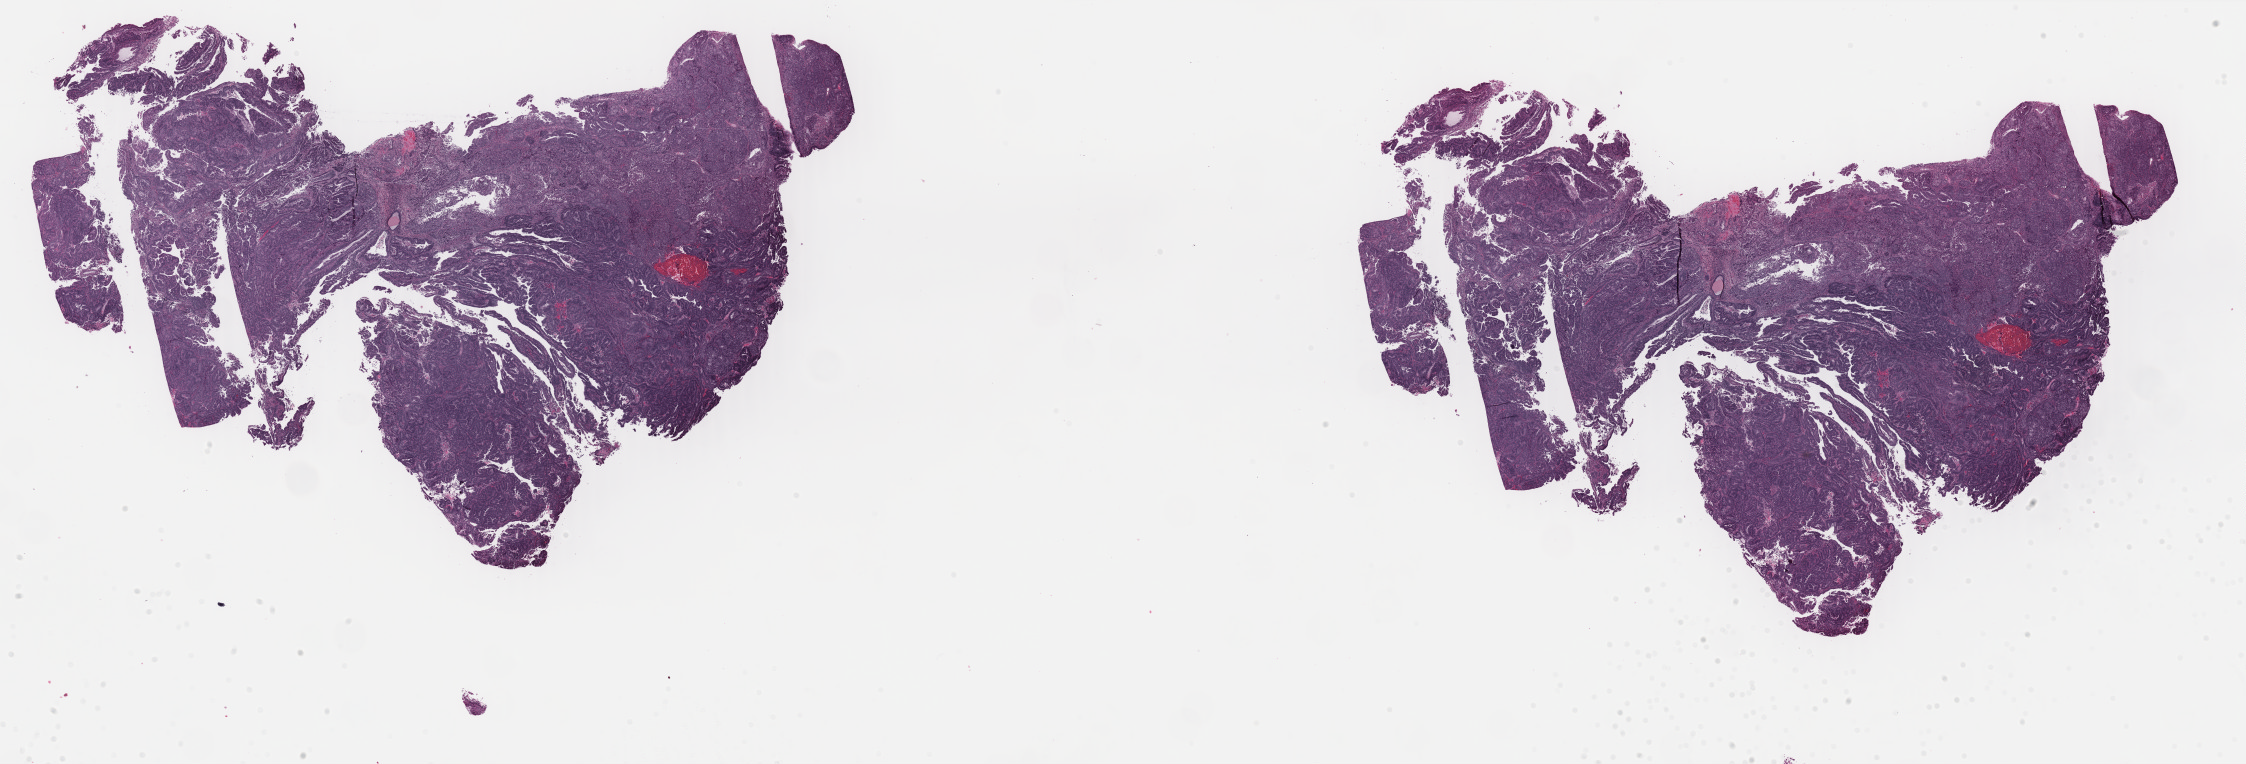
Hematoxylin and eosin (H&E) stained whole-slide image, a low-resolution overview of the entire scanned area, about 35.5 x 12.1 mm, formalin-fixed paraffin-embedded (FFPE) diagnostic section, uterus, primary tumour sample. Female patient; age at initial diagnosis 87 years. Histologic grade: G3 (poorly differentiated).
FIGO stage: II. Diagnosis: Endometrioid adenocarcinoma, NOS (endometrium).